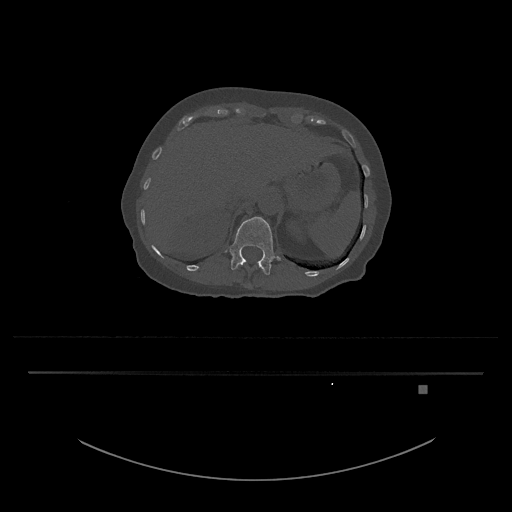
CT including the spine, one axial slice. Slice 569 of 797 in the series (ordered by position). Reconstruction kernel Br40s/3. Bone window (W 1800 / L 400 HU). 0.5 mm slice thickness. 512 × 512 image matrix. Patient: female, 57 years. Case-level facts recorded for this patient, not image findings: primary cancer: cervical.
Annotated regions visible in this slice (semi-automatic segmentation, software-assisted and operator-edited):
- L1 vertebra: bounding box (x1, y1, x2, y2) in pixels: (224, 217, 281, 275)
- T12 vertebra: (242, 262, 264, 272)